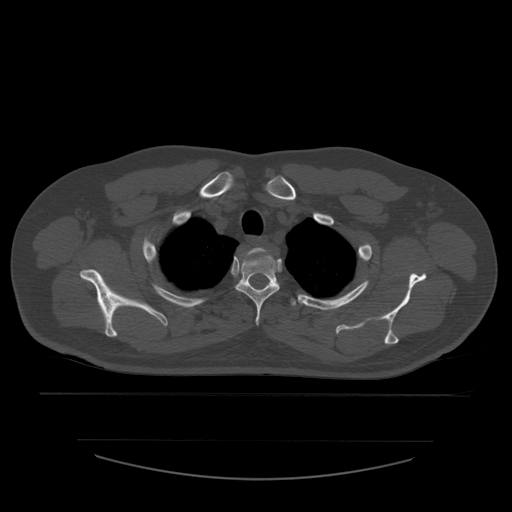
CT including the spine, one axial slice. Position 451 of 532 along the scan axis. Reconstruction kernel STANDARD. 120 kVp. Bone window (W 1800 / L 400 HU). 512 × 512 image matrix, field of view 441 × 441 mm. Patient age 44 years. Case-level facts recorded for this patient, not image findings: primary cancer: soft tissue sarcoma.
Annotated regions visible in this slice (semi-automatic segmentation, software-assisted and operator-edited):
- T1 vertebra: bounding box [x1, y1, x2, y2] px = [239, 248, 266, 267]
- T2 vertebra: [236, 251, 280, 326]
- T3 vertebra: [291, 299, 297, 306]